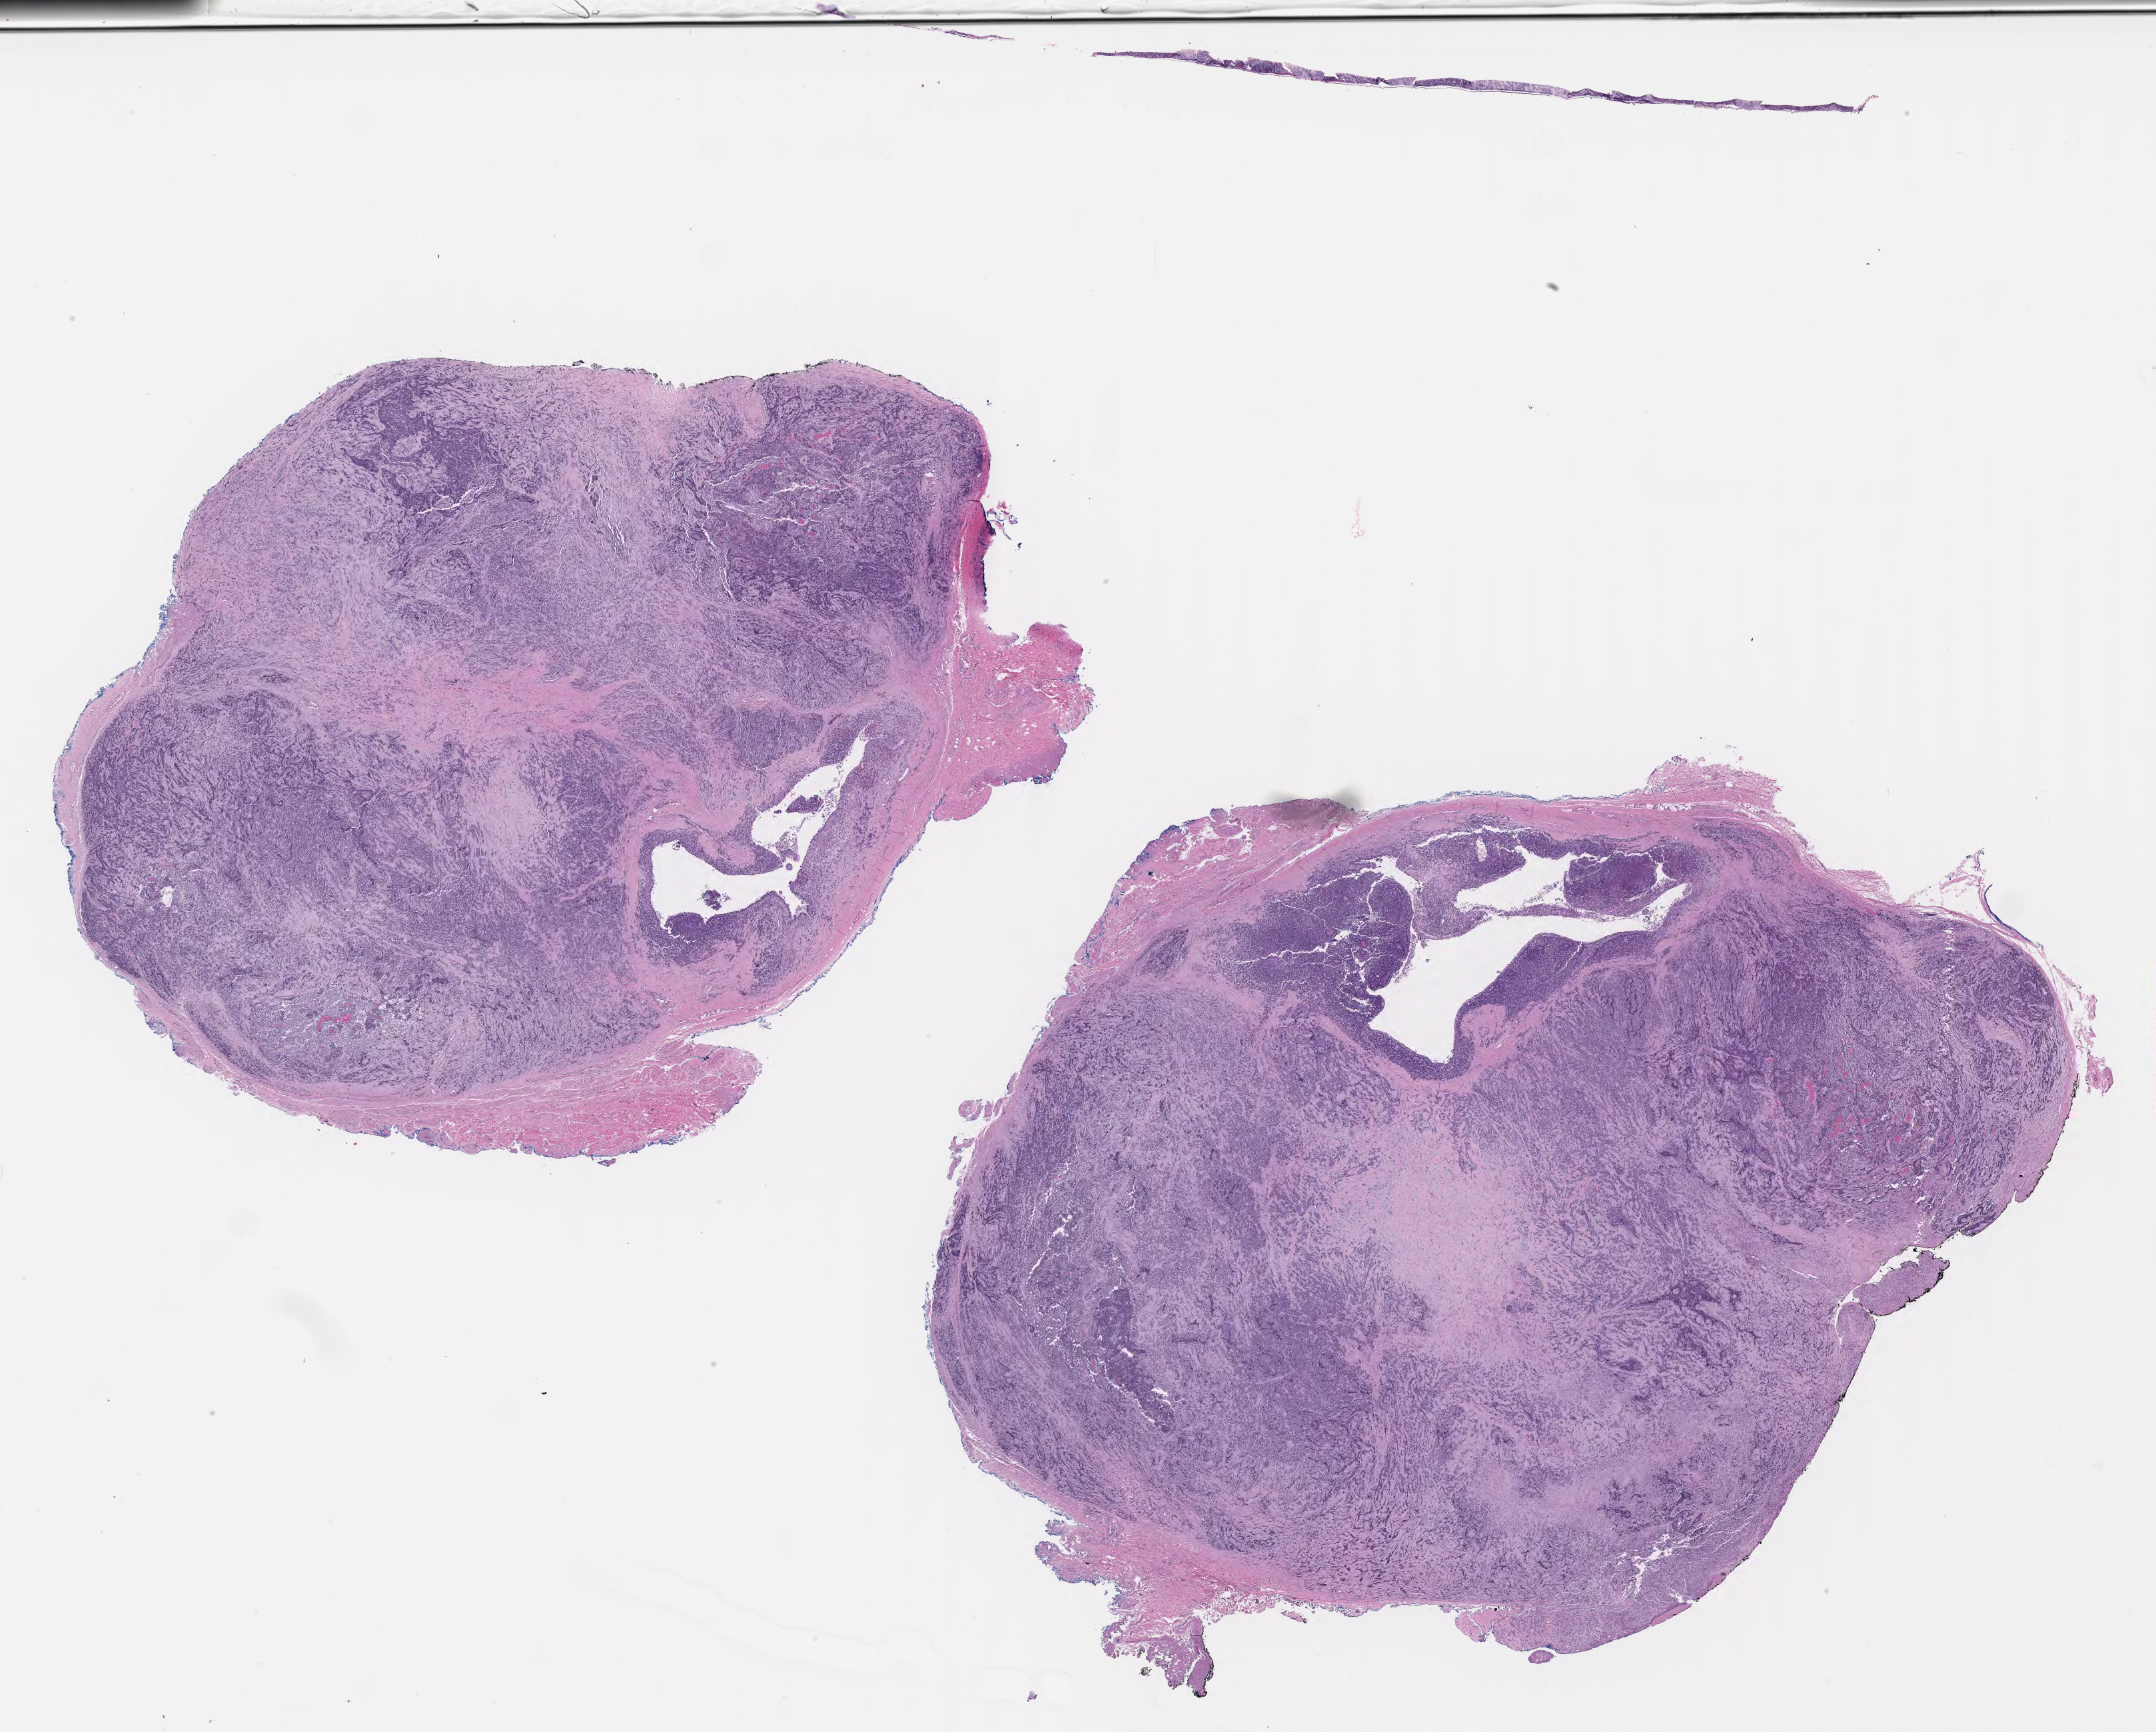
Haematoxylin and eosin whole-slide image of tumor tissue from the head and neck, shown as a low-resolution overview of the whole scanned area (about 26.2 x 21.0 mm); formalin-fixed paraffin-embedded section. Patient: male, age 427 days.
• diagnosis (ICD-O-3 morphology term): Embryonal rhabdomyosarcoma, NOS